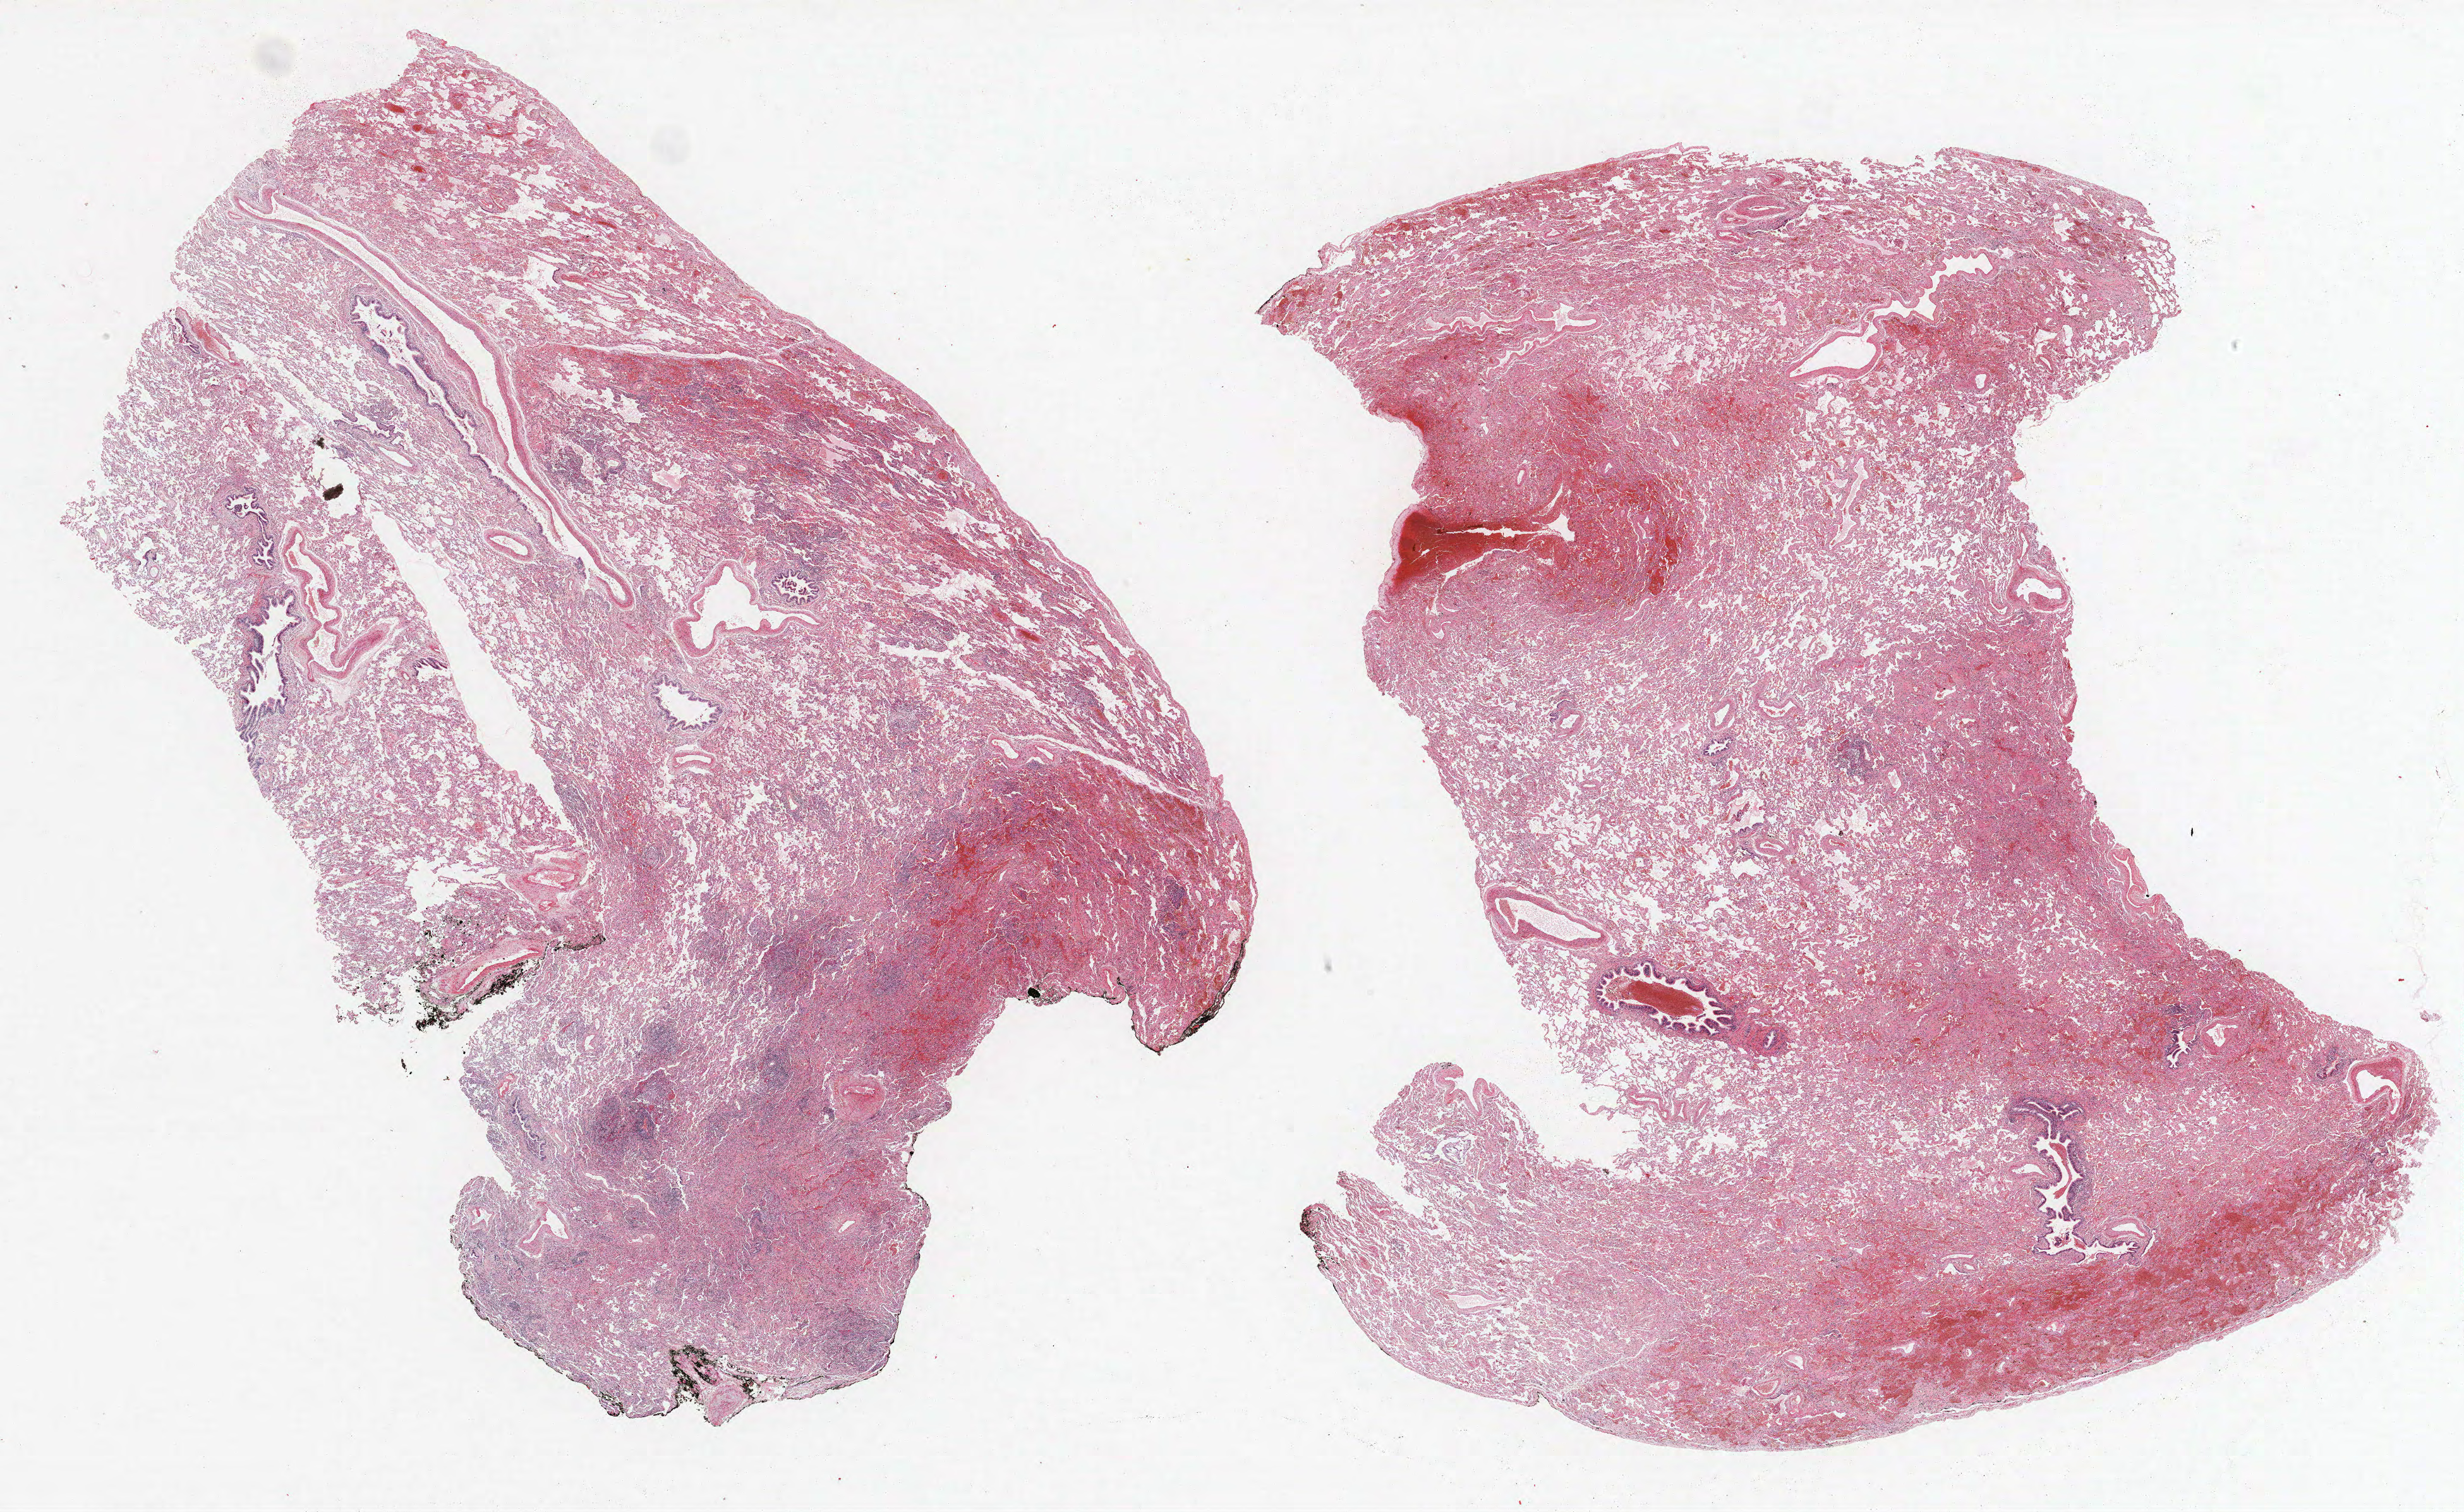
Whole-slide histology image, H&E-stained, a low-resolution overview of the entire scanned area, about 31.2 x 19.1 mm. Formalin-fixed paraffin-embedded (FFPE) section. Lung. Female, age 59 at enrolment. Former smoker at enrolment. Grade: well differentiated (G1).
Stage (AJCC 6th edition): IA. Primary tumour location (clinical record): right lower lobe. Participant's lung-cancer diagnosis: Bronchiolo-alveolar carcinoma, mucinous. Tumour size (pathology): 15 mm.